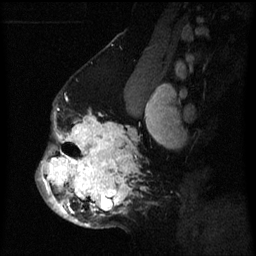
Breast MRI (dynamic contrast-enhanced), one sagittal slice; slice 40 of 60 in the series (ordered by position); dynamic contrast-enhanced series, image 2 of 3 at this slice position (ordered by acquisition); 1.5 T; TE 4.2 ms, TR 8 ms; 2 mm slice thickness; 256 × 256 image matrix. Female patient, age 50 years.
Annotated regions visible in this slice (semi-automatically segmented with operator editing):
- analysis volume of interest (the breast-tissue region the enhancement analysis was run in; not a lesion): box from (x=36, y=108) to (x=151, y=228) px
- tumour enhancement mask (voxels above the 70 % enhancement threshold inside the analysis volume of interest): (x=40, y=111)–(x=150, y=227)